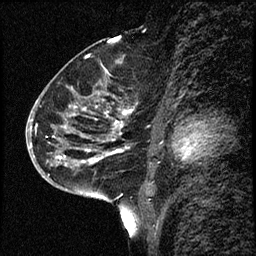
Breast MRI (dynamic contrast-enhanced), one sagittal slice. Slice 36 of 68 in the series (ordered by position). Dynamic contrast-enhanced study with each time point stored as its own series, time point 2 of 3 at this slice position (early post-contrast, ordered by acquisition time). 1.5 T. TE 4.2 ms, TR 17.6 ms. 2 mm slice thickness. 256 × 256 image matrix, field of view 200 × 200 mm. Female patient, age 52 years. From the clinical record (not read from this slice): setting: breast cancer imaged before/during neoadjuvant chemotherapy; receptor status: HER2-positive.
Structures marked on this image (semi-automatic segmentation, software-assisted and operator-edited):
- analysis volume of interest (the breast-tissue region the enhancement analysis was run in; not a lesion): bounding box (x1, y1, x2, y2) in pixels: (50, 61, 146, 184)
- tumour enhancement mask (voxels above the 100 % enhancement threshold inside the analysis volume of interest): (57, 106, 129, 164)